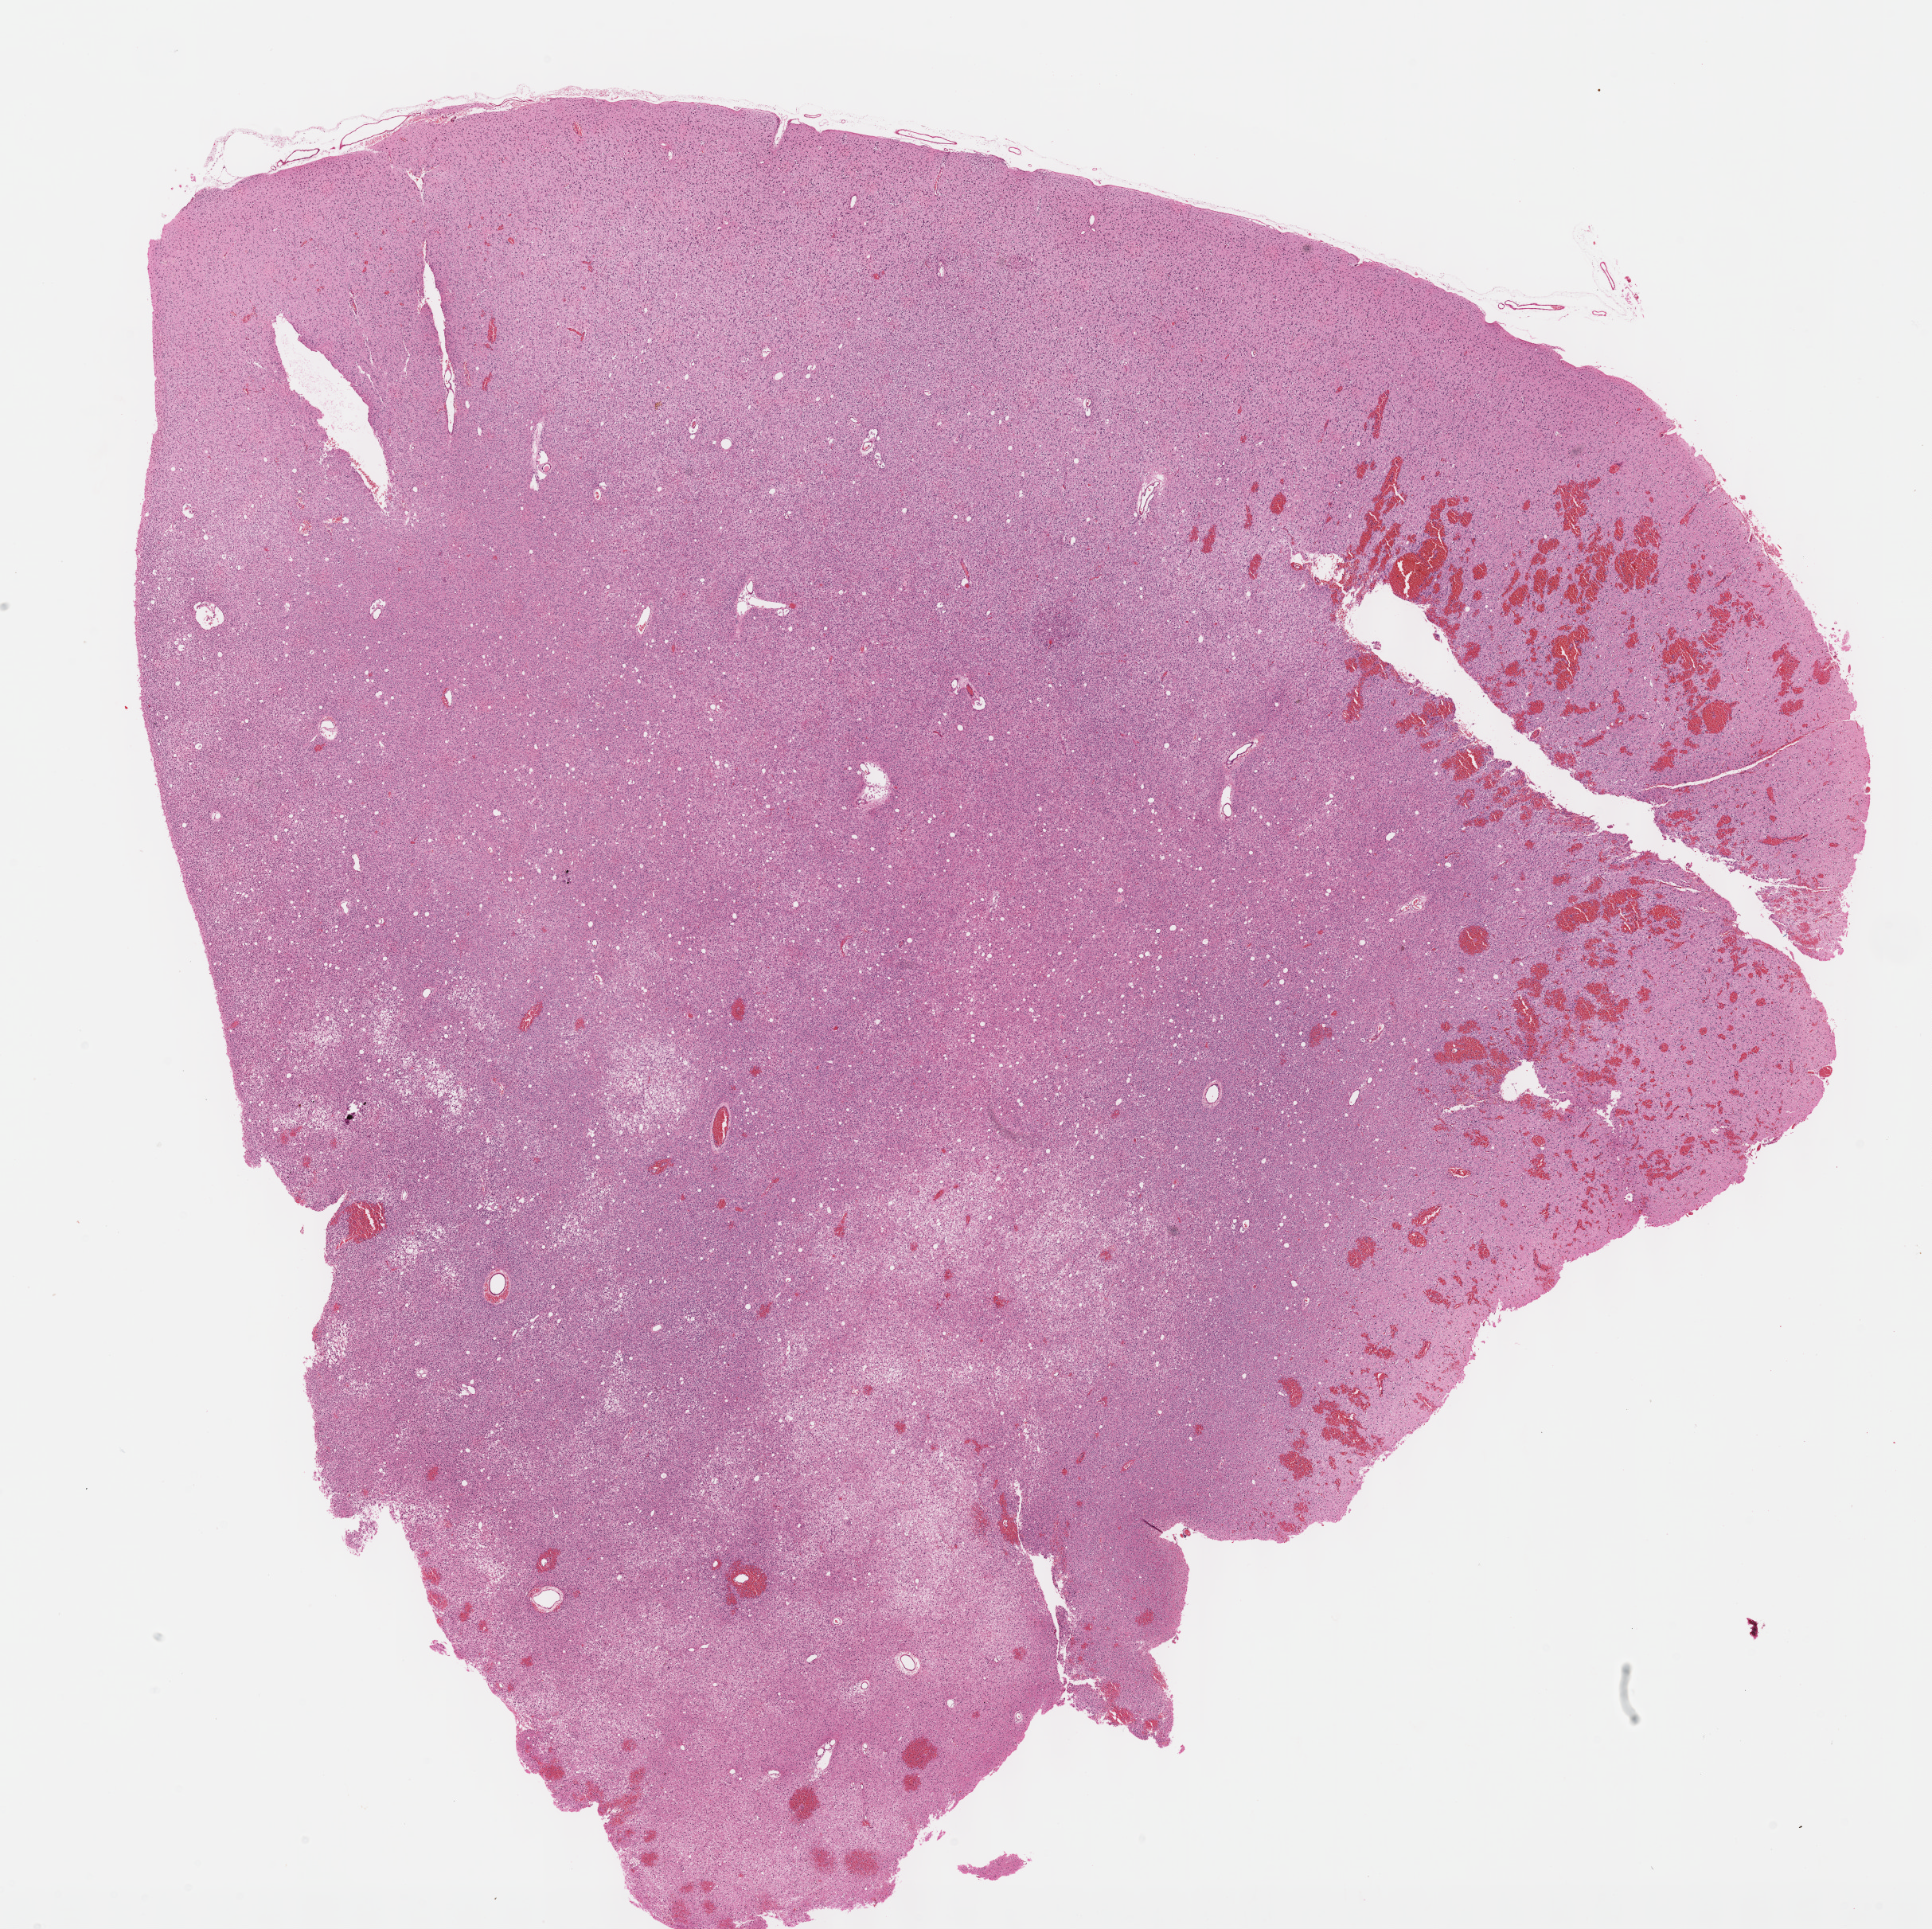
Hematoxylin and eosin (H&E) stained whole-slide image — a low-resolution overview of the entire scanned area, about 19.6 x 19.6 mm (slide scanned at 40x), FFPE section, sample: primary tumour, brain. Female, age 25 years at initial diagnosis. Histologic grade: G2 (moderately differentiated).
- diagnosis: Oligodendroglioma, NOS (cerebrum)